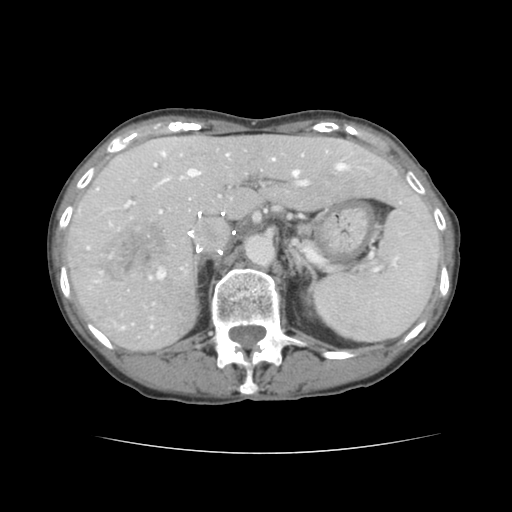
Contrast-enhanced abdominal CT, one axial slice; slice 93 of 136 in the series (ordered by position); 120 kVp; intravenous contrast given; soft-tissue window (W 400 / L 40 HU); 2.5 mm slice thickness; 512 × 512 image matrix, field of view 319 × 319 mm. Female patient, age 77 years. From the clinical record (not read from this slice): diagnosis: colorectal cancer liver metastases, imaged before liver resection; multiple liver metastases: yes.
Annotated regions visible in this slice (manually delineated by an expert):
- hepatic veins: bounding box [x1, y1, x2, y2] px = [122, 153, 345, 329]
- liver: [68, 136, 427, 351]
- planned liver remnant (the part of the liver to remain after resection): [153, 136, 428, 218]
- portal vein (with intrahepatic branches): [97, 164, 311, 279]
- liver metastasis: [98, 222, 170, 282]